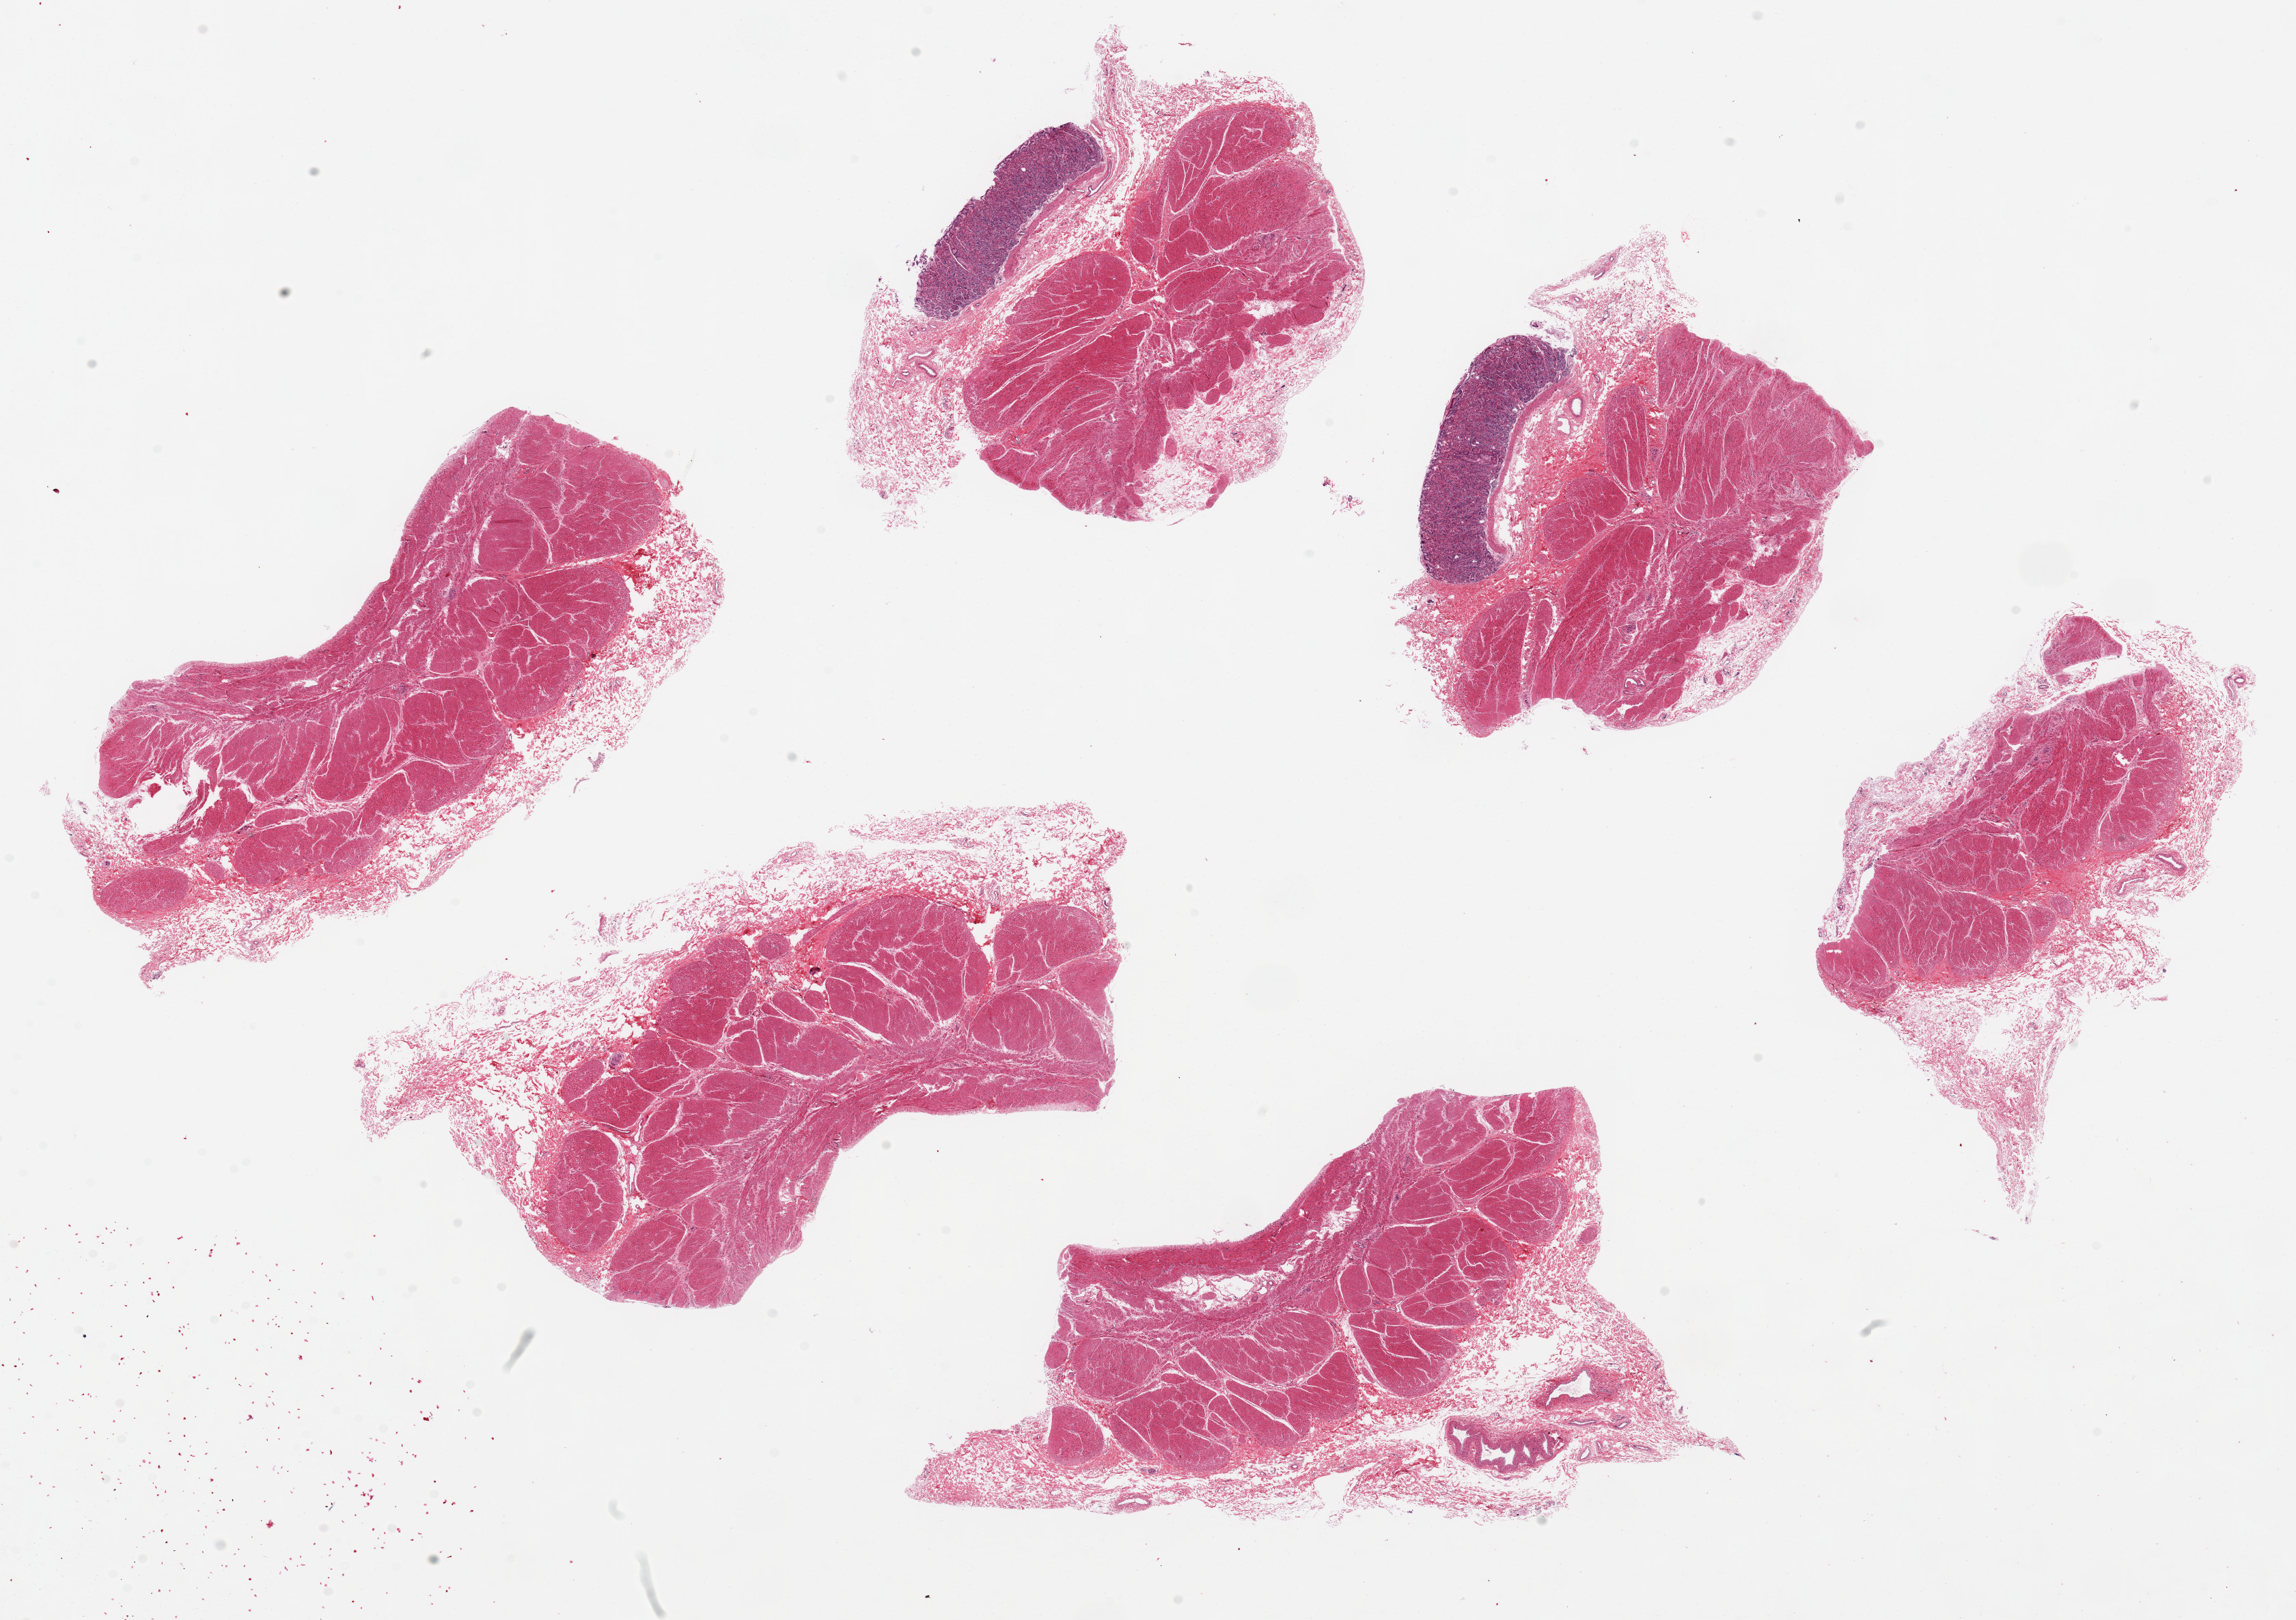
H&E whole-slide image, whole scanned area (about 26.6 x 18.8 mm) shown as a low-resolution overview, PAXgene-fixed, paraffin-embedded tissue, sampled site (target tissue): stomach, donor tissue sample. Donor sex: male.
• pathologist's review note for this sample: 6 pieces, ~7x4.5mm. Very good mucosal (0.87mm) preservation in 2 pieces; none in others